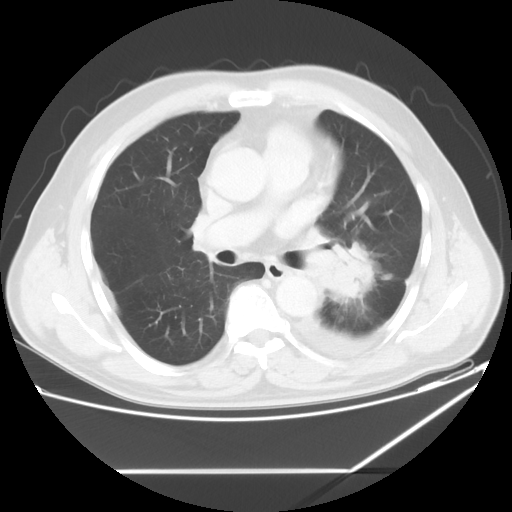
Chest CT, one axial slice; slice 33 of 60 in the series (ordered by position); reconstruction kernel STANDARD; 120 kVp; lung window (W 1500 / L -600 HU); 5 mm slice thickness; 512 × 512 image matrix. Male patient, age 62 years. Case-level facts recorded for this patient, not image findings: clinical TNM (as recorded): T3 N0 M1.
Annotated regions visible in this slice (bounding box drawn by a radiologist):
- lung tumour (recorded histology: adenocarcinoma): bounding box (x1, y1, x2, y2) in pixels: (314, 241, 378, 301)
- lung tumour (recorded histology: adenocarcinoma): (328, 238, 375, 303)